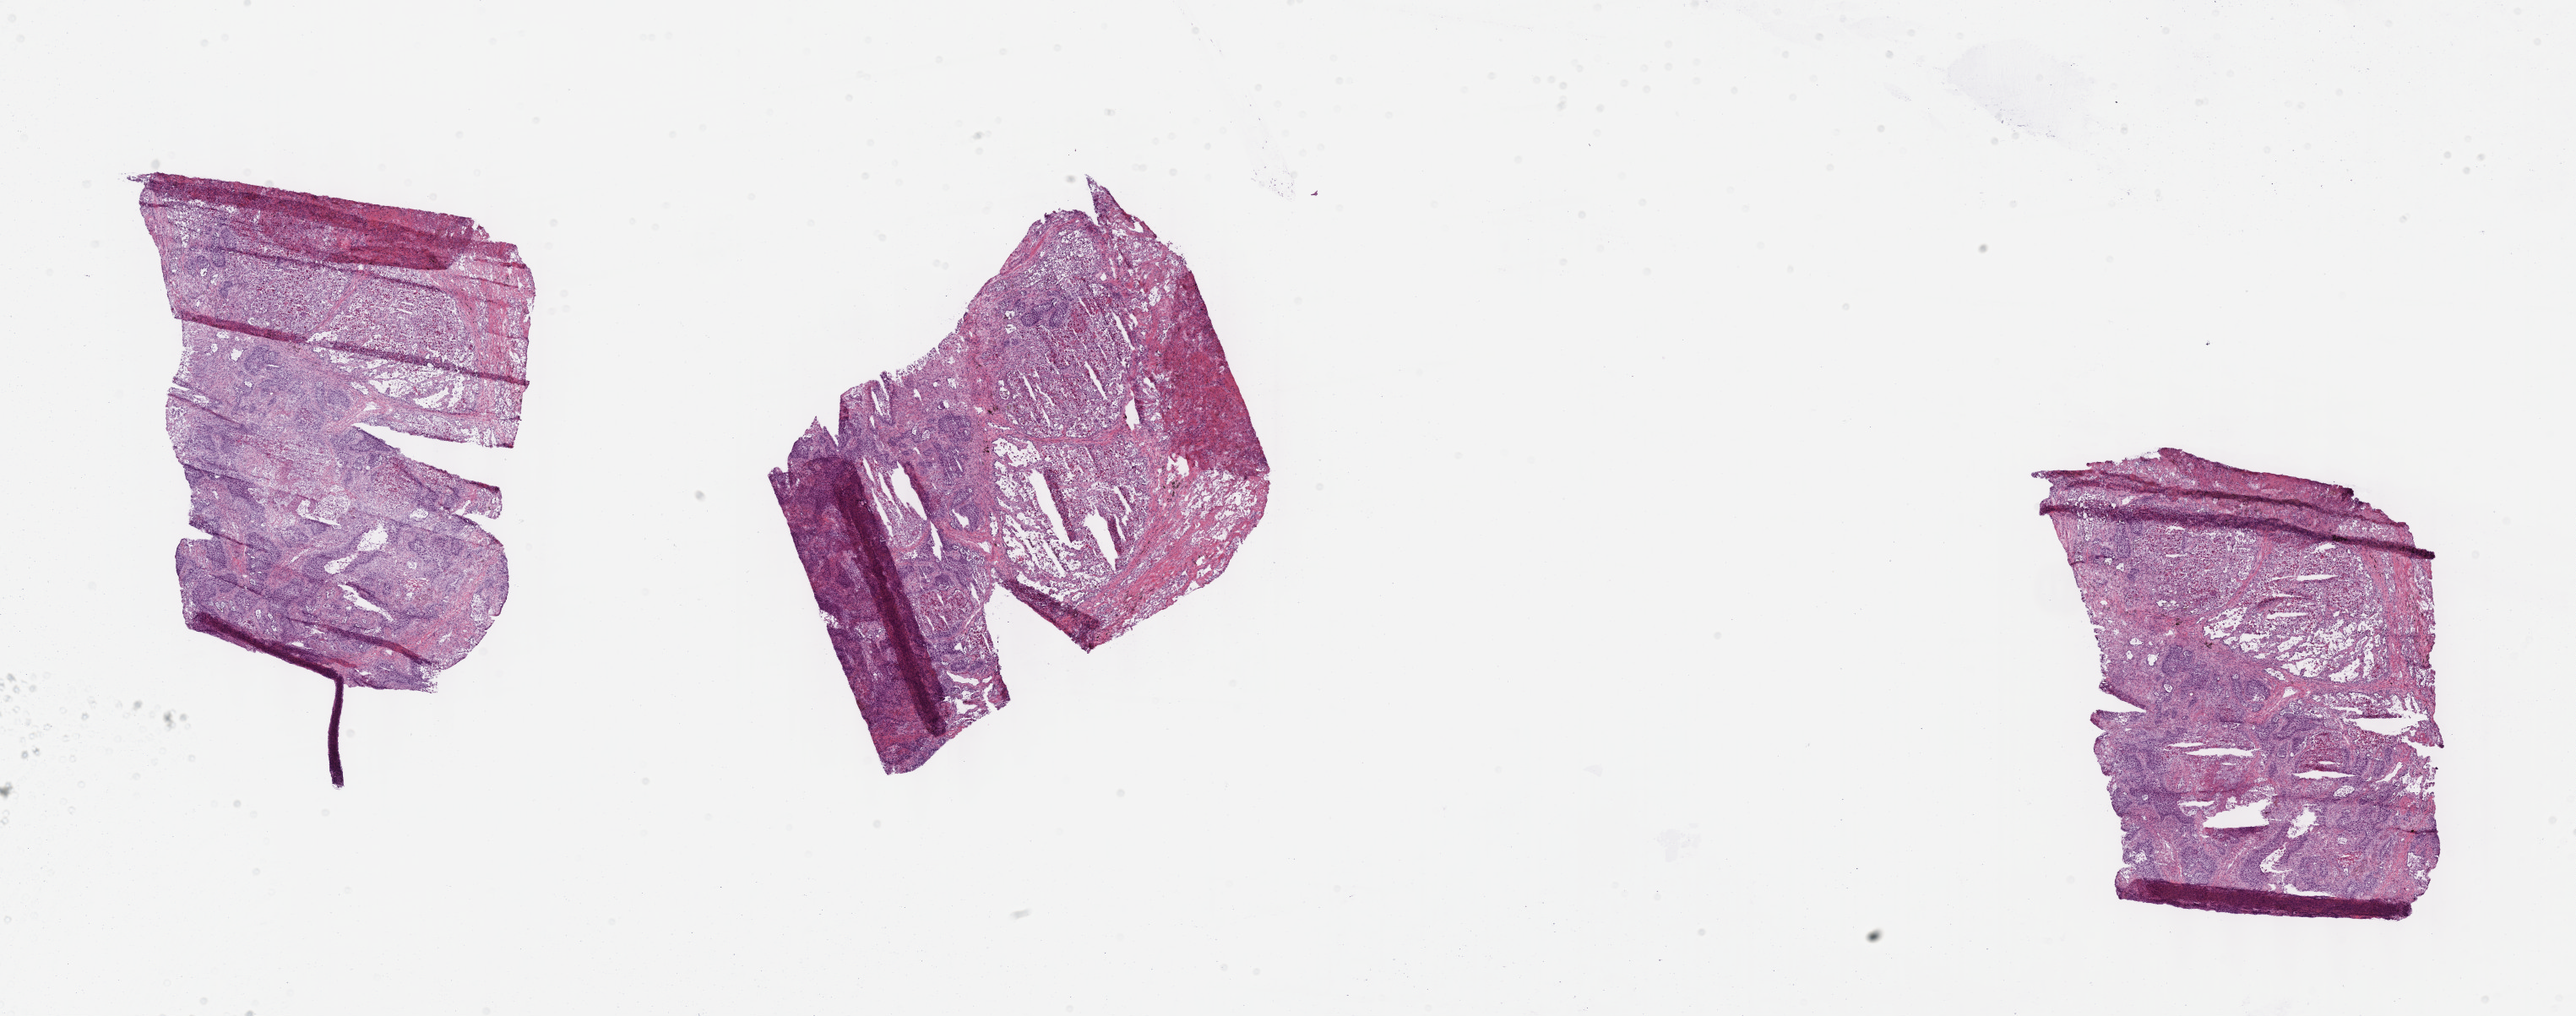
Hematoxylin and eosin (H&E) stained whole-slide image — whole scanned area (about 24.6 x 9.7 mm, slide scanned at 40x) shown as a low-resolution overview. Frozen section. Lung, primary tumour sample. Patient: female, age at initial diagnosis 55 years. Composition of this section per pathologist review: tumour cells 90%, tumour nuclei 65%, normal cells 0%, stromal cells 10%, necrosis 0%. Inflammatory infiltration, as recorded: lymphocyte infiltration 10%, monocyte infiltration 5%, neutrophil infiltration 5%.
AJCC pathologic stage: IA. TNM: T1b N0 M0. Histologic diagnosis: Adenocarcinoma, NOS (upper lobe, lung).